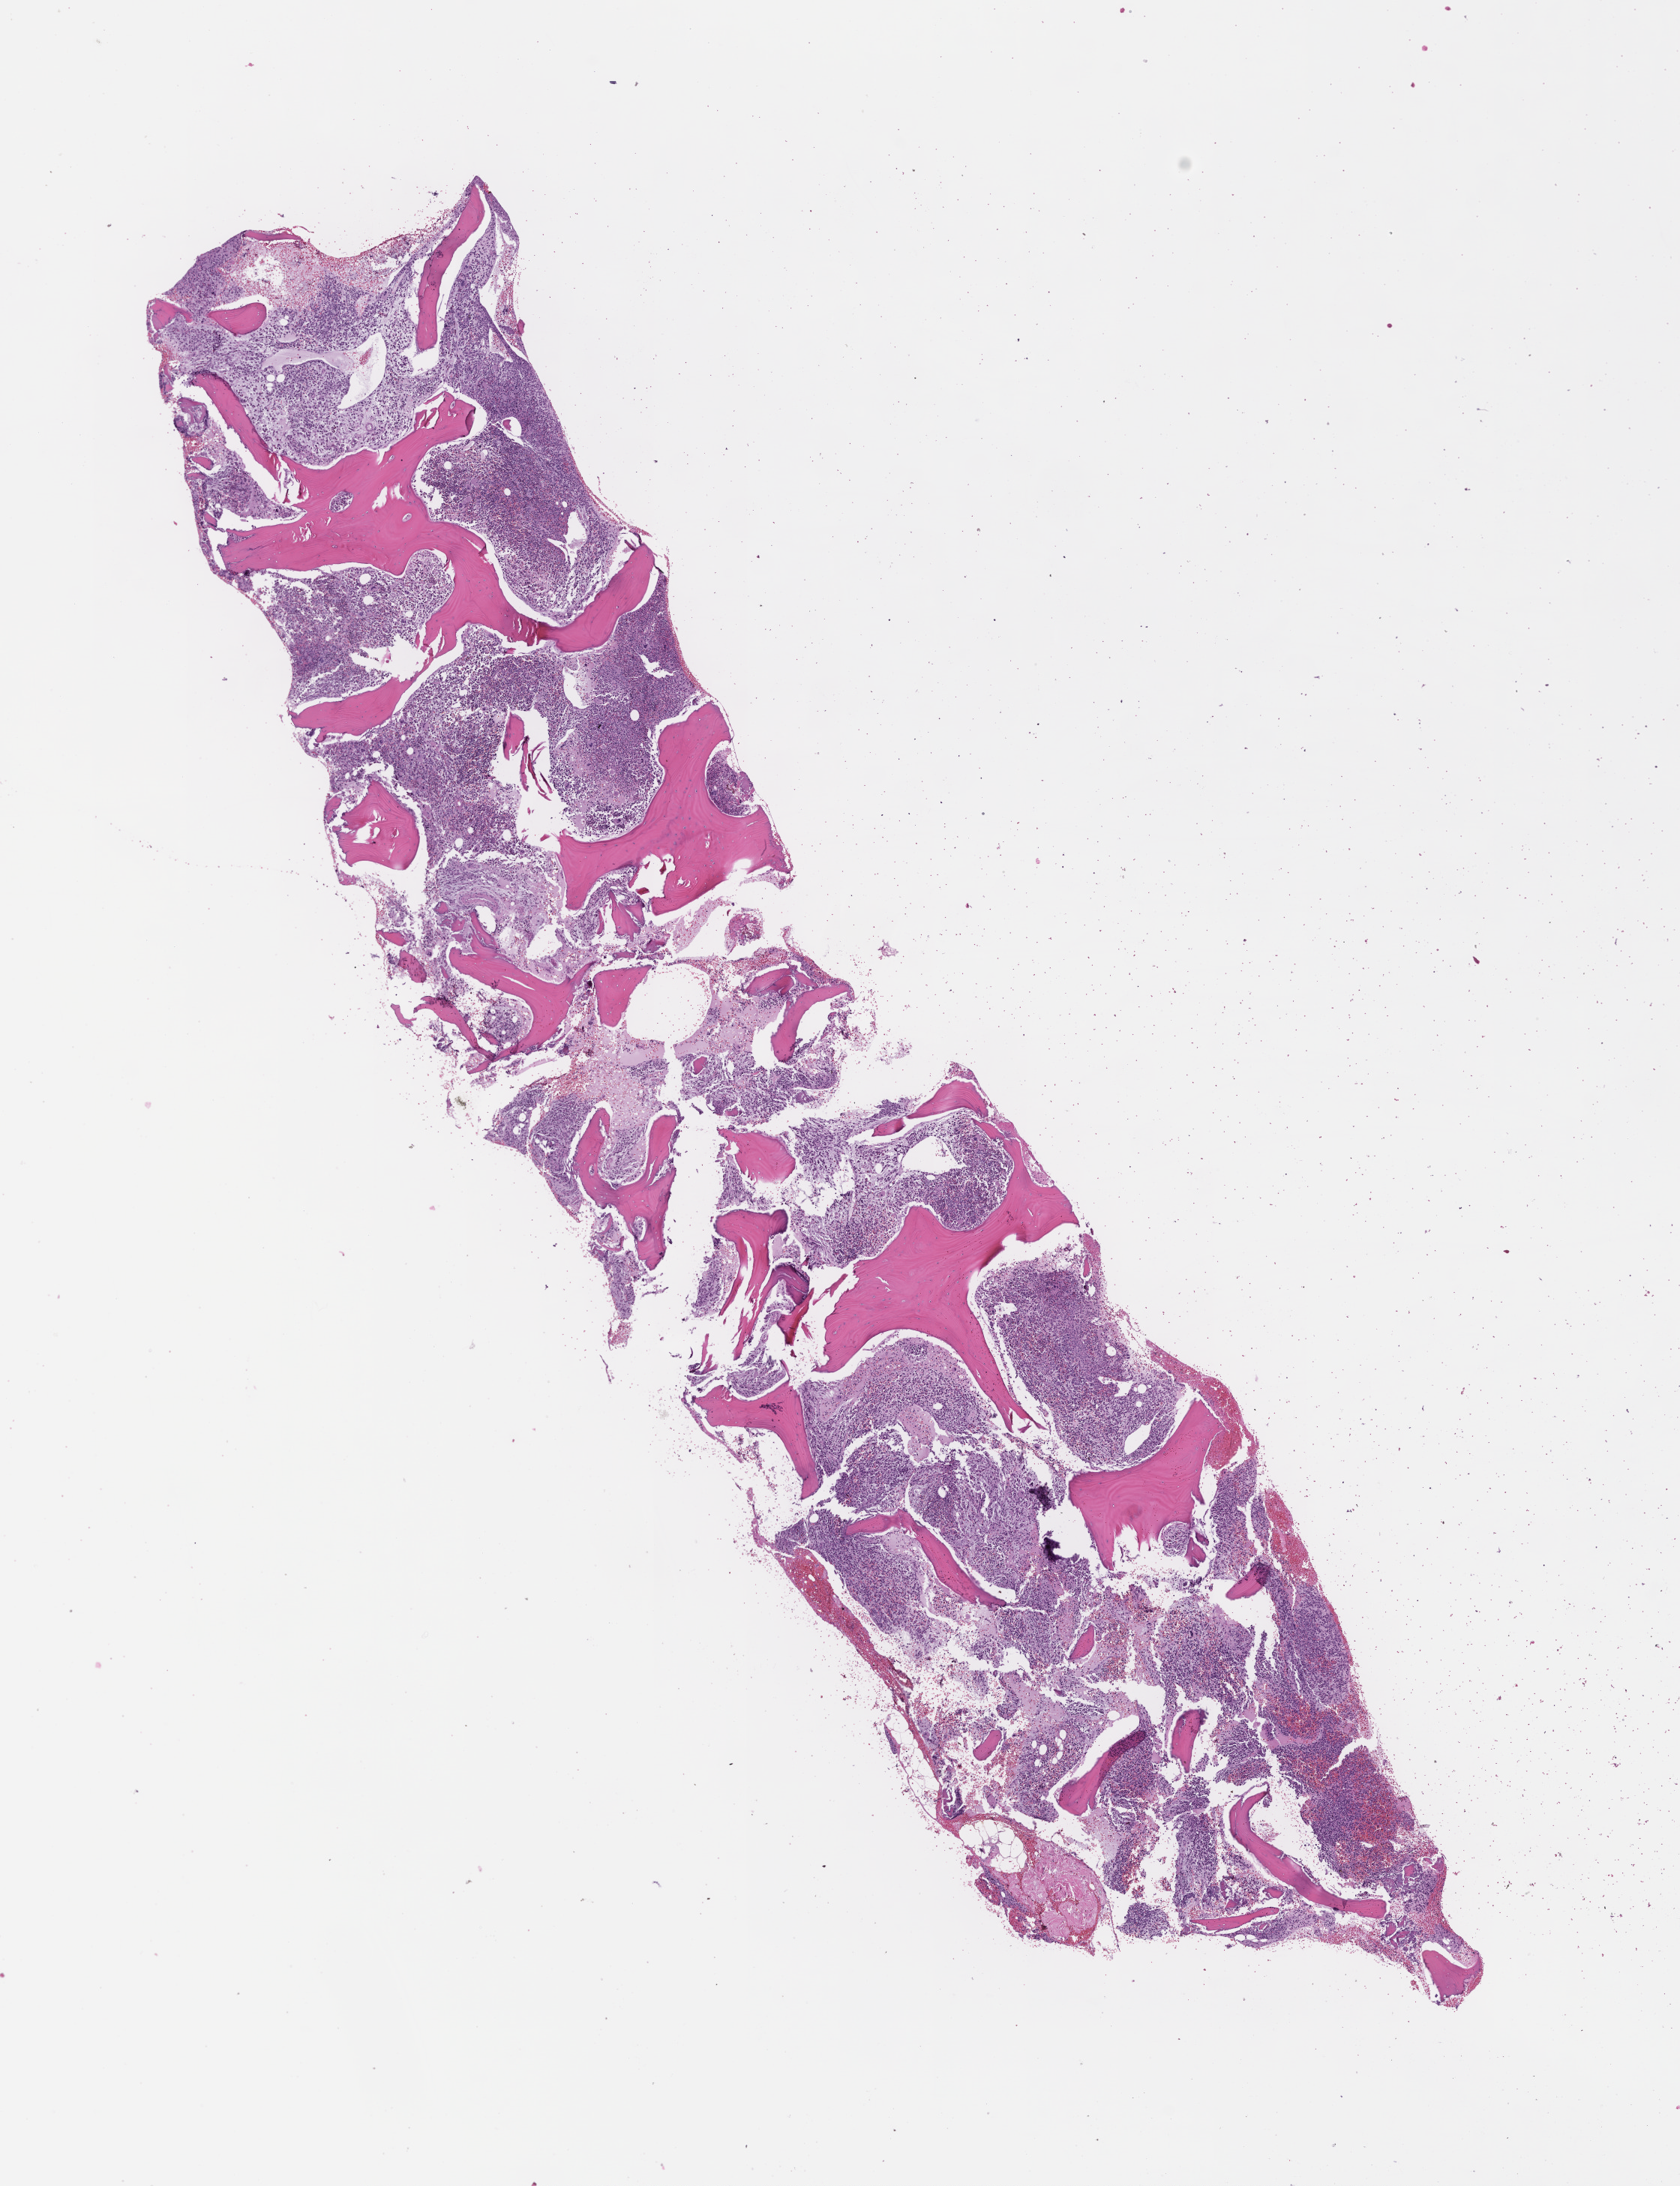
Digitized hematoxylin and eosin (H&E)-stained section — low-resolution overview of the scanned area, about 9.0 x 11.8 mm. Formalin-fixed paraffin-embedded section. Site: bone. Patient sex: female.
This section: primary tumour tissue. Diagnosis: Plasma Cell Myeloma.